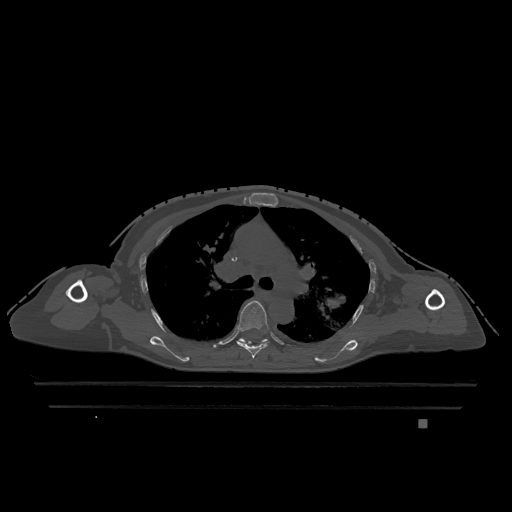
CT including the spine, one axial slice. Position 825 of 1317 along the scan axis. Bone window (W 1800 / L 400 HU). 512 × 512 image matrix. Female patient, age 74 years. From the clinical record (not read from this slice): primary cancer: lung.
Annotated regions visible in this slice (semi-automatically segmented with operator editing):
- T5 vertebra: bounding box <237,300,269,359> (left, top, right, bottom; pixels)
- T6 vertebra: <238,338,268,344>